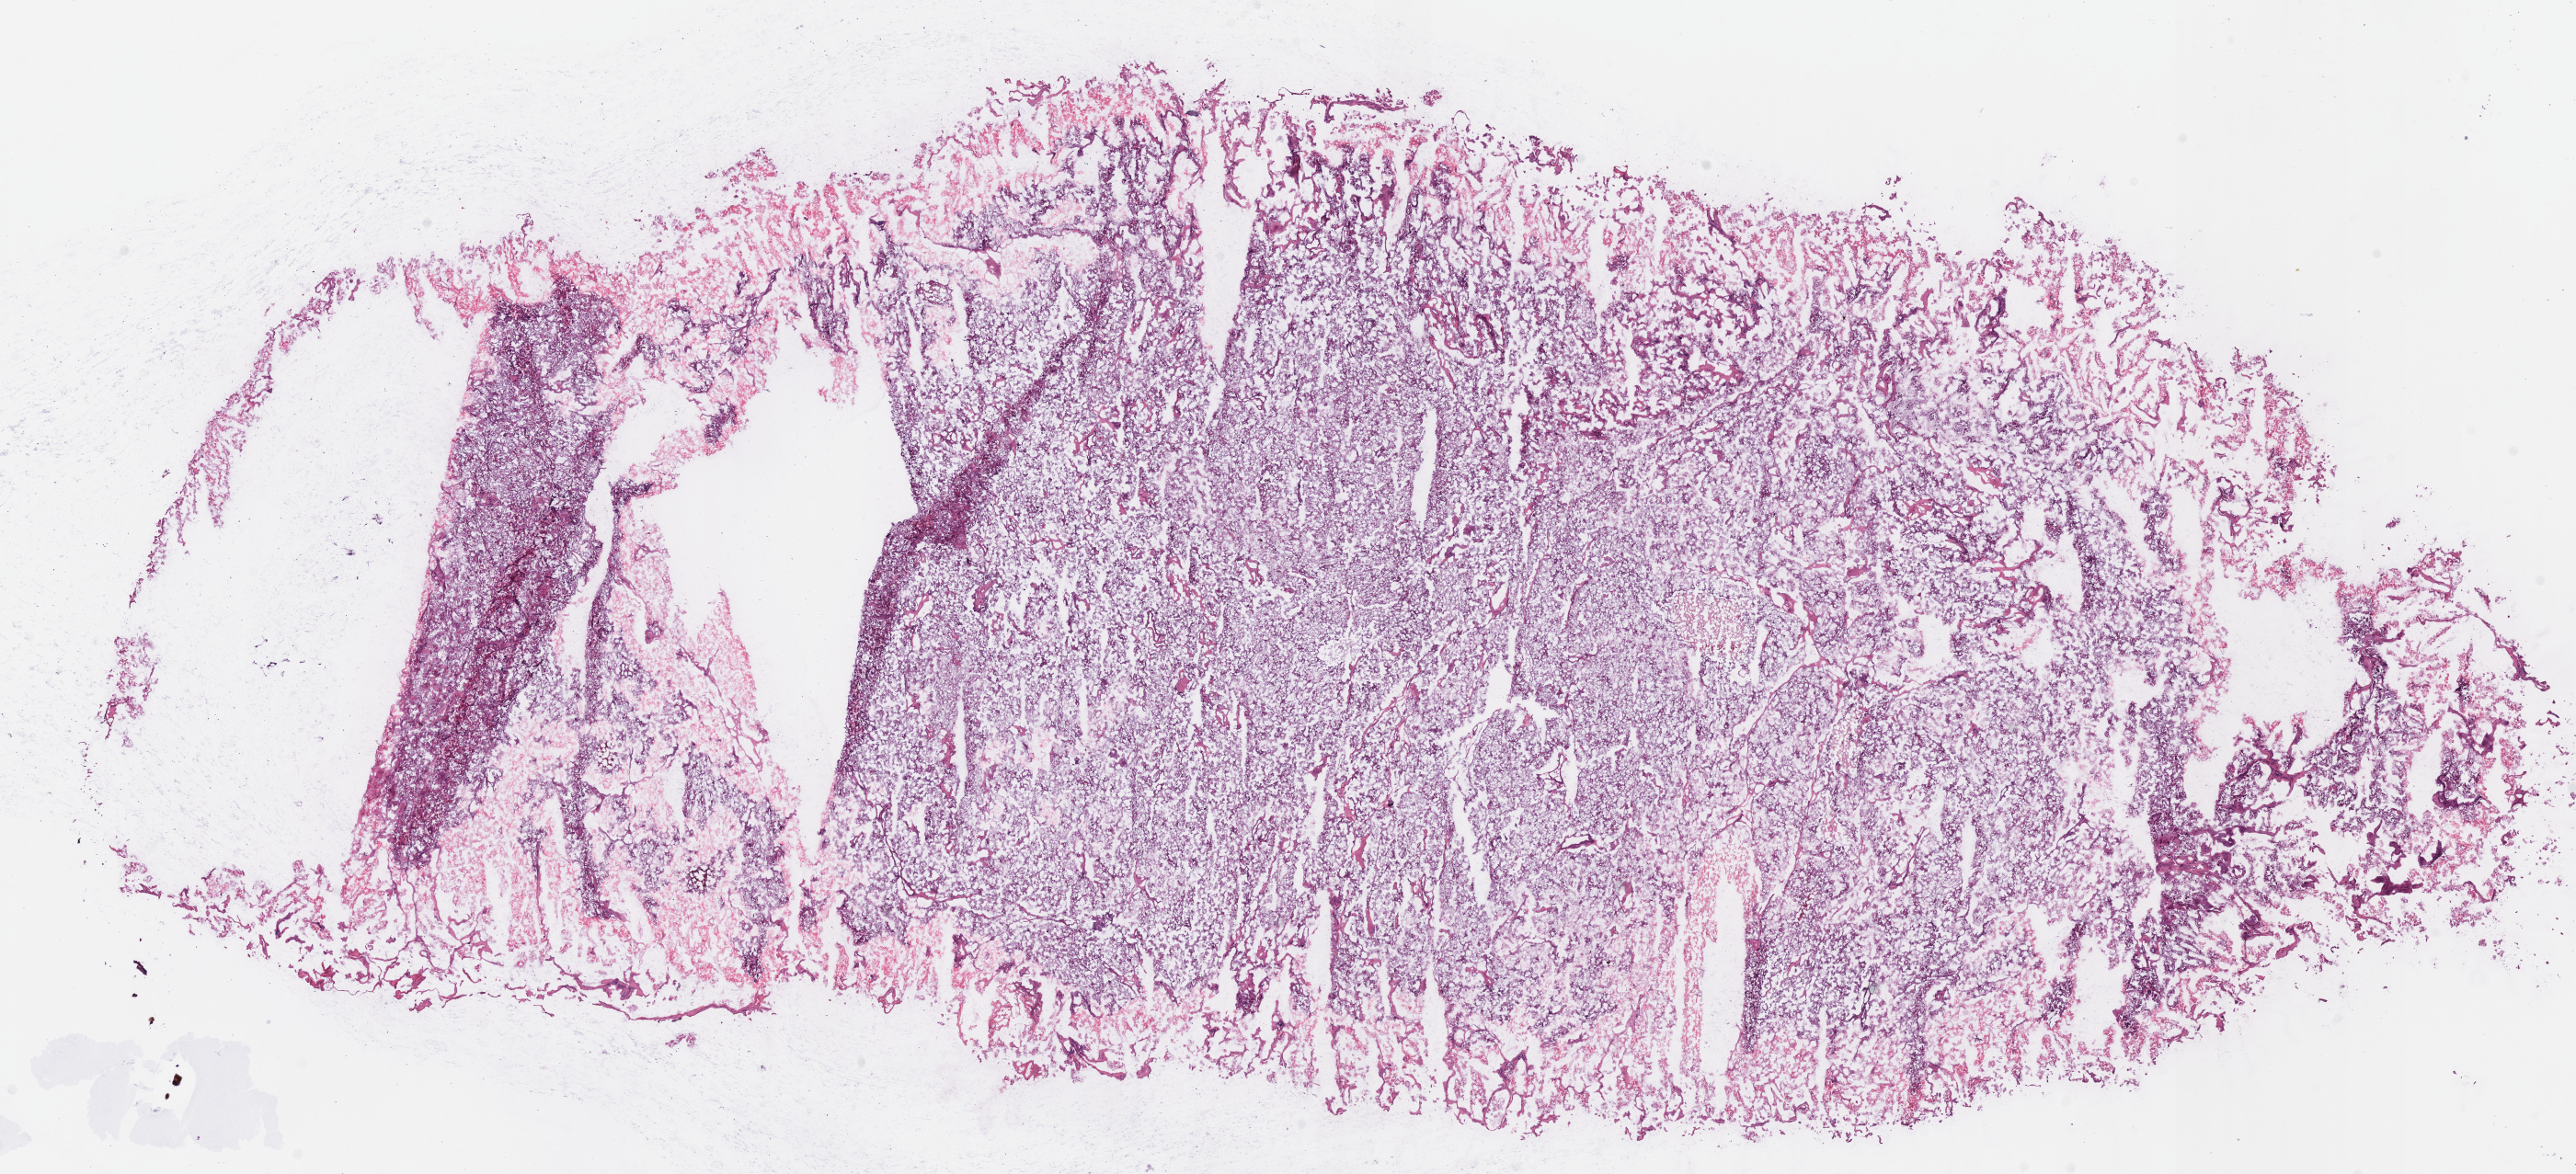
Digitized H&E tissue section (whole slide) — a low-resolution overview of the entire scanned area, about 22.0 x 10.0 mm (from a 40x scan); frozen section from the bottom of the tissue portion; sample: primary tumour, kidney. Male patient; age at initial diagnosis 49 years. Composition of this section per pathologist review: tumour cells 95%, tumour nuclei 90%, normal cells 0%, stromal cells 5%, necrosis 0%.
Pathologic diagnosis: Renal cell carcinoma, chromophobe type. AJCC pathologic stage: I (7th edition).